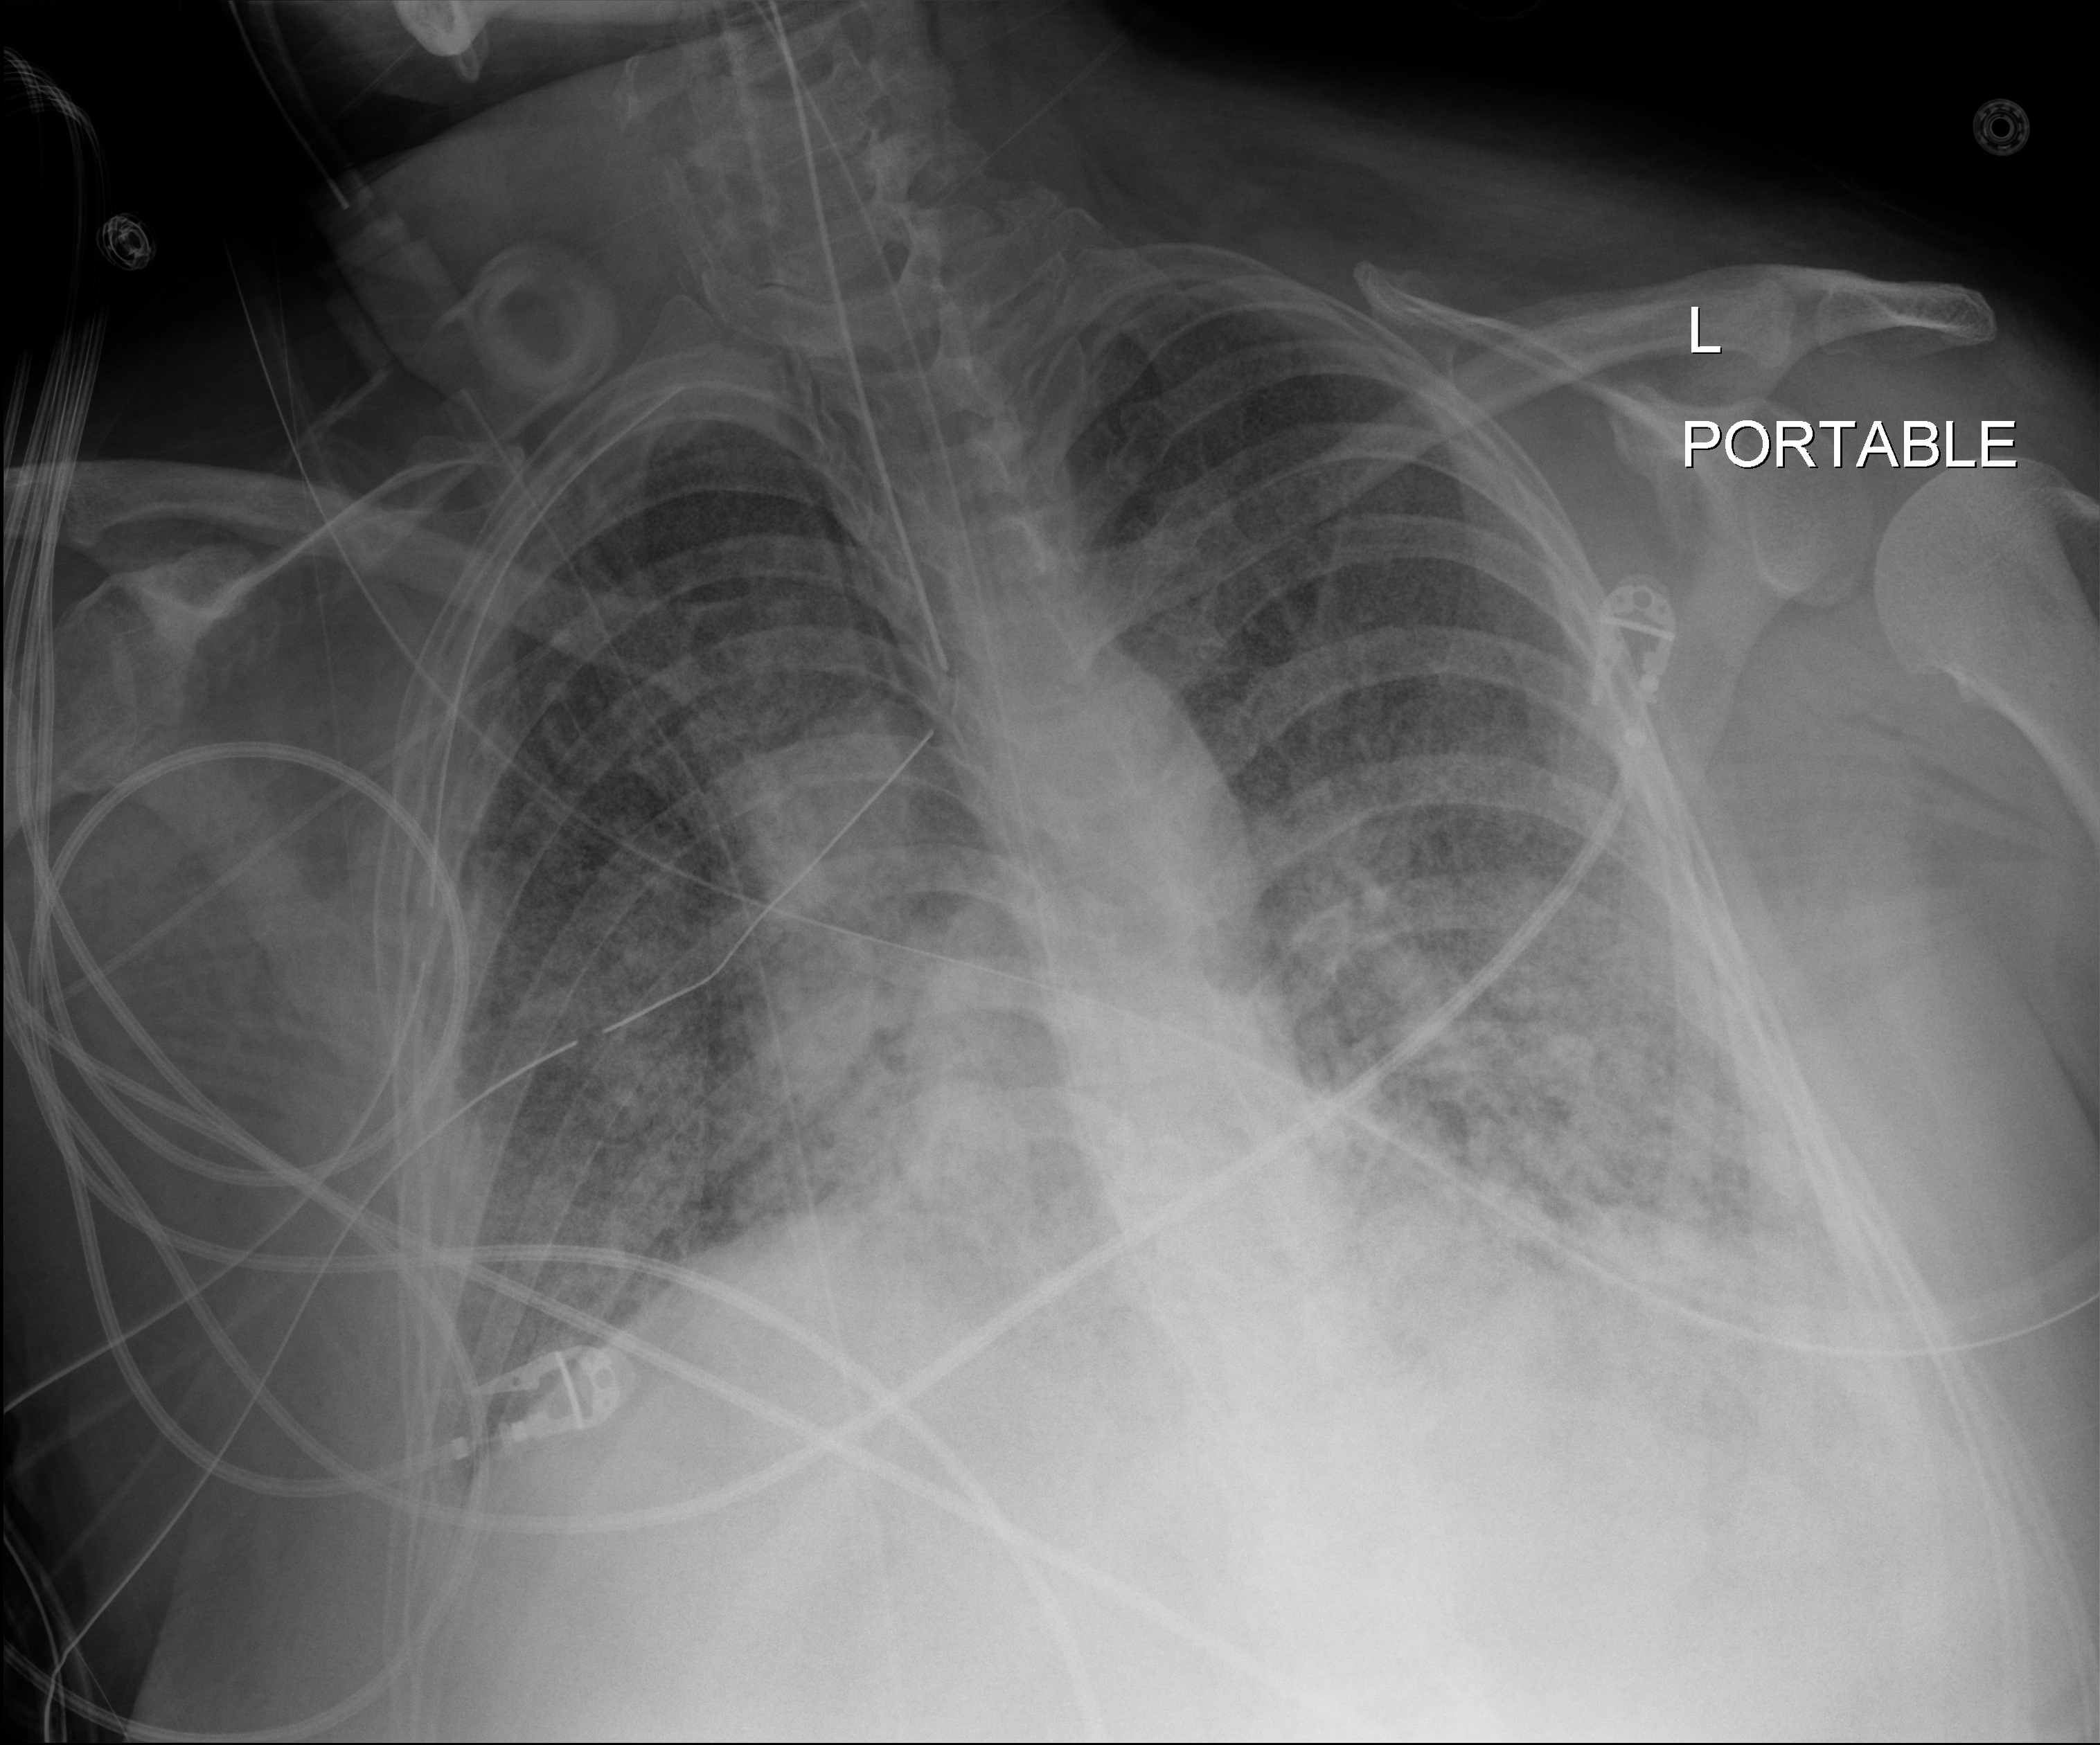
Chest X-ray (portable), anteroposterior (AP) projection. Patient hospitalised with COVID-19, aged 18–59 years.
Admission-level facts for this patient (not findings on this image; timing relative to this image not recorded): admitted to intensive care during this hospital stay: yes; mechanically ventilated during this hospital stay: yes; length of hospital stay: 48 days.